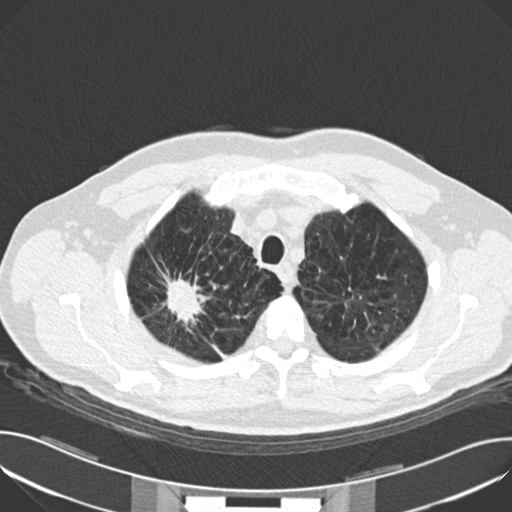
Low-dose screening chest CT, one axial slice; position 136 of 159 along the scan axis; 120 kVp; lung window (W 1500 / L -600 HU); 2 mm slice thickness; 512 × 512 image matrix, field of view 380 × 380 mm.
Annotated regions visible in this slice (manually delineated by an expert):
- lesion 1 (tumor, upper lobe of right lung): bounding box <165,278,202,323> (left, top, right, bottom; pixels)